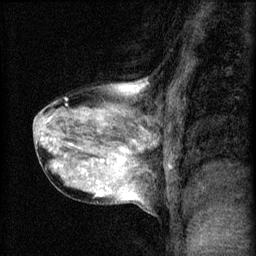
Breast MRI (dynamic contrast-enhanced), one sagittal slice. Slice 29 of 60 in the series (ordered by position). 3 images stored at this slice position (order not interpretable as contrast timing). 1.5 T. TE 4.2 ms, TR 8.2 ms. 2 mm slice thickness. 256 × 256 image matrix, field of view 180 × 180 mm. Female patient, age 40 years.
Outlined on this slice (semi-automatic segmentation, software-assisted and operator-edited):
- analysis volume of interest (the breast-tissue region the enhancement analysis was run in; not a lesion): bounding box (x1, y1, x2, y2) in pixels: (32, 80, 167, 207)
- tumour enhancement mask (voxels above the 70 % enhancement threshold inside the analysis volume of interest): (42, 88, 137, 197)